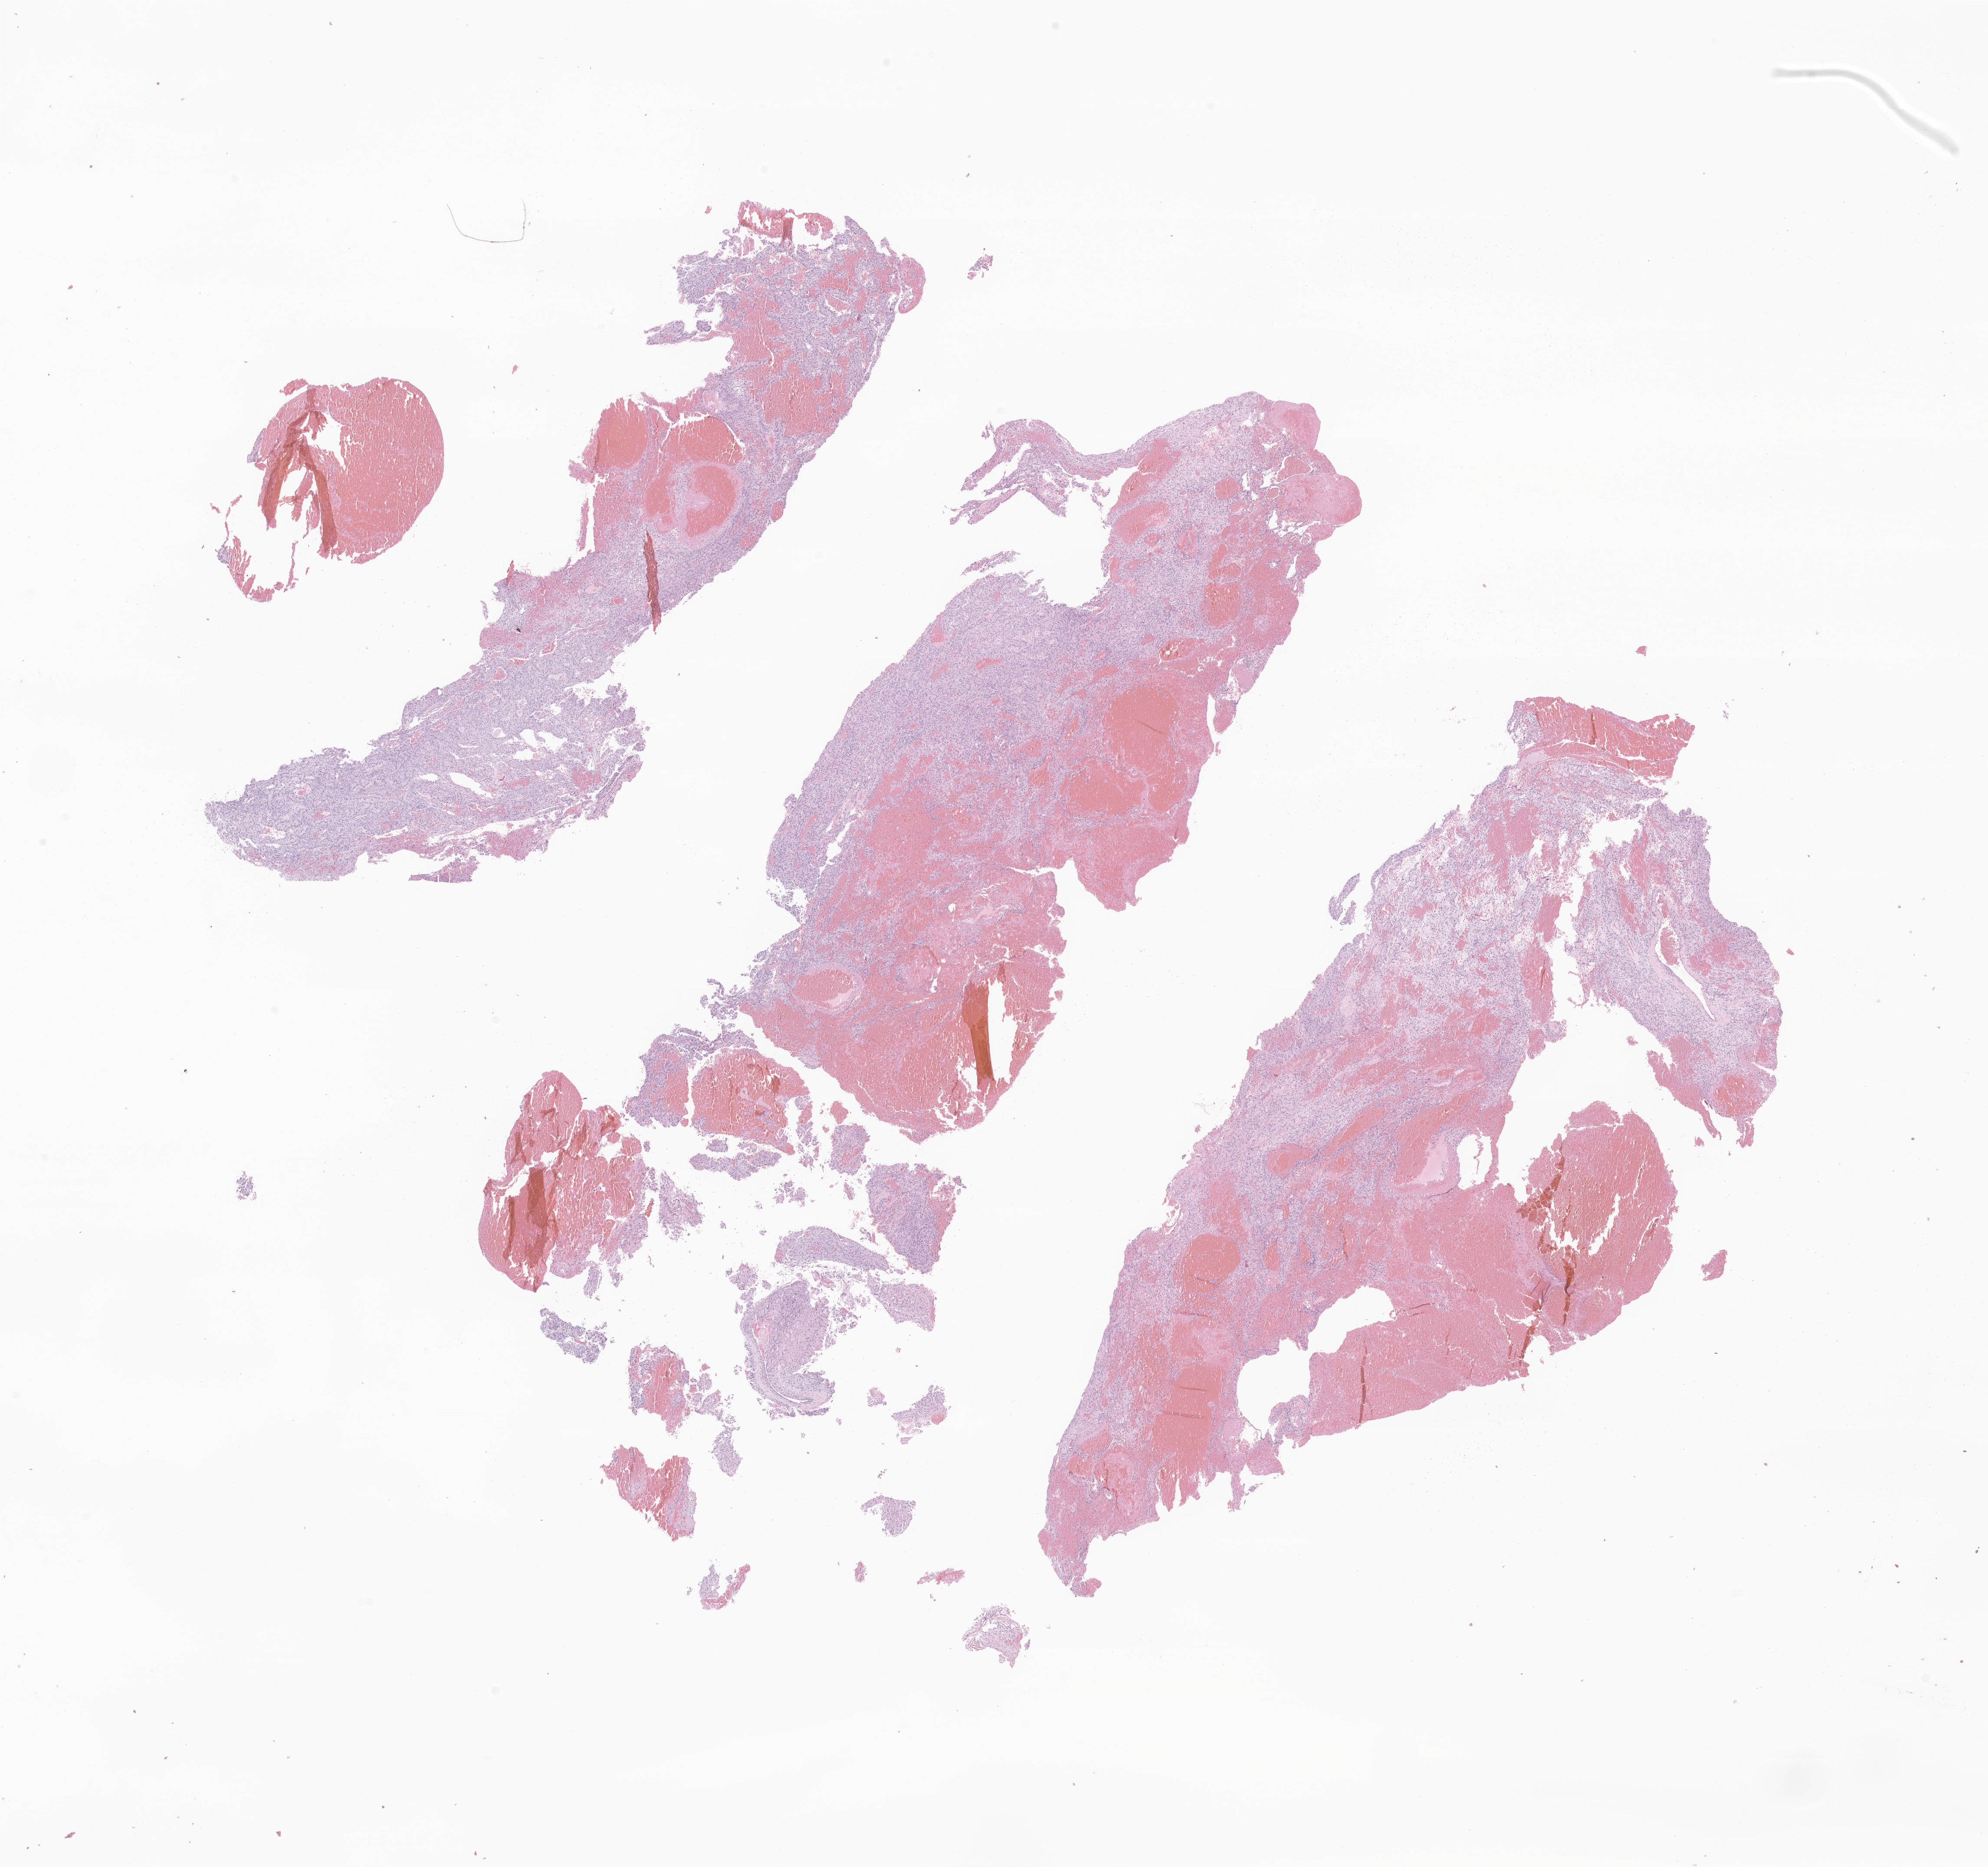
Digitized hematoxylin and eosin (H&E)-stained section of tumor tissue from the brain, low-resolution overview of the scanned area, about 19.3 x 18.1 mm, formalin-fixed paraffin-embedded section. Patient: male, age 145 months (12 years 1 month).
Recorded diagnosis: Neoplasm, malignant.